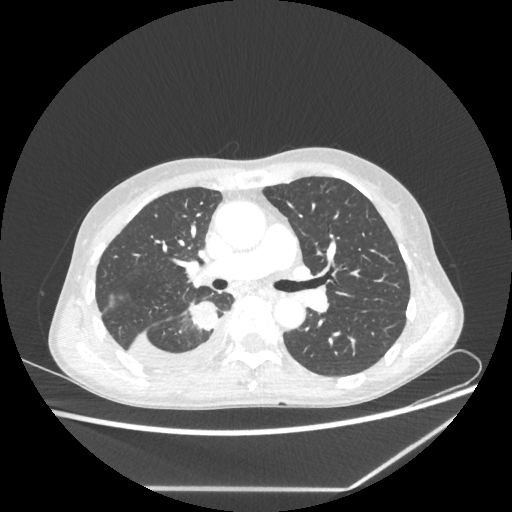
Chest CT, one axial slice; slice 137 of 237 in the series (ordered by position); reconstruction kernel STANDARD; 80 kVp; lung window (W 1500 / L -600 HU); 512 × 512 image matrix. Patient: female, 59 years. From the clinical record (not read from this slice): clinical TNM (as recorded): T1c N1 M1.
Structures marked on this image (bounding box drawn by a radiologist):
- lung tumour (recorded histology: adenocarcinoma): box from (x=188, y=299) to (x=218, y=336) px